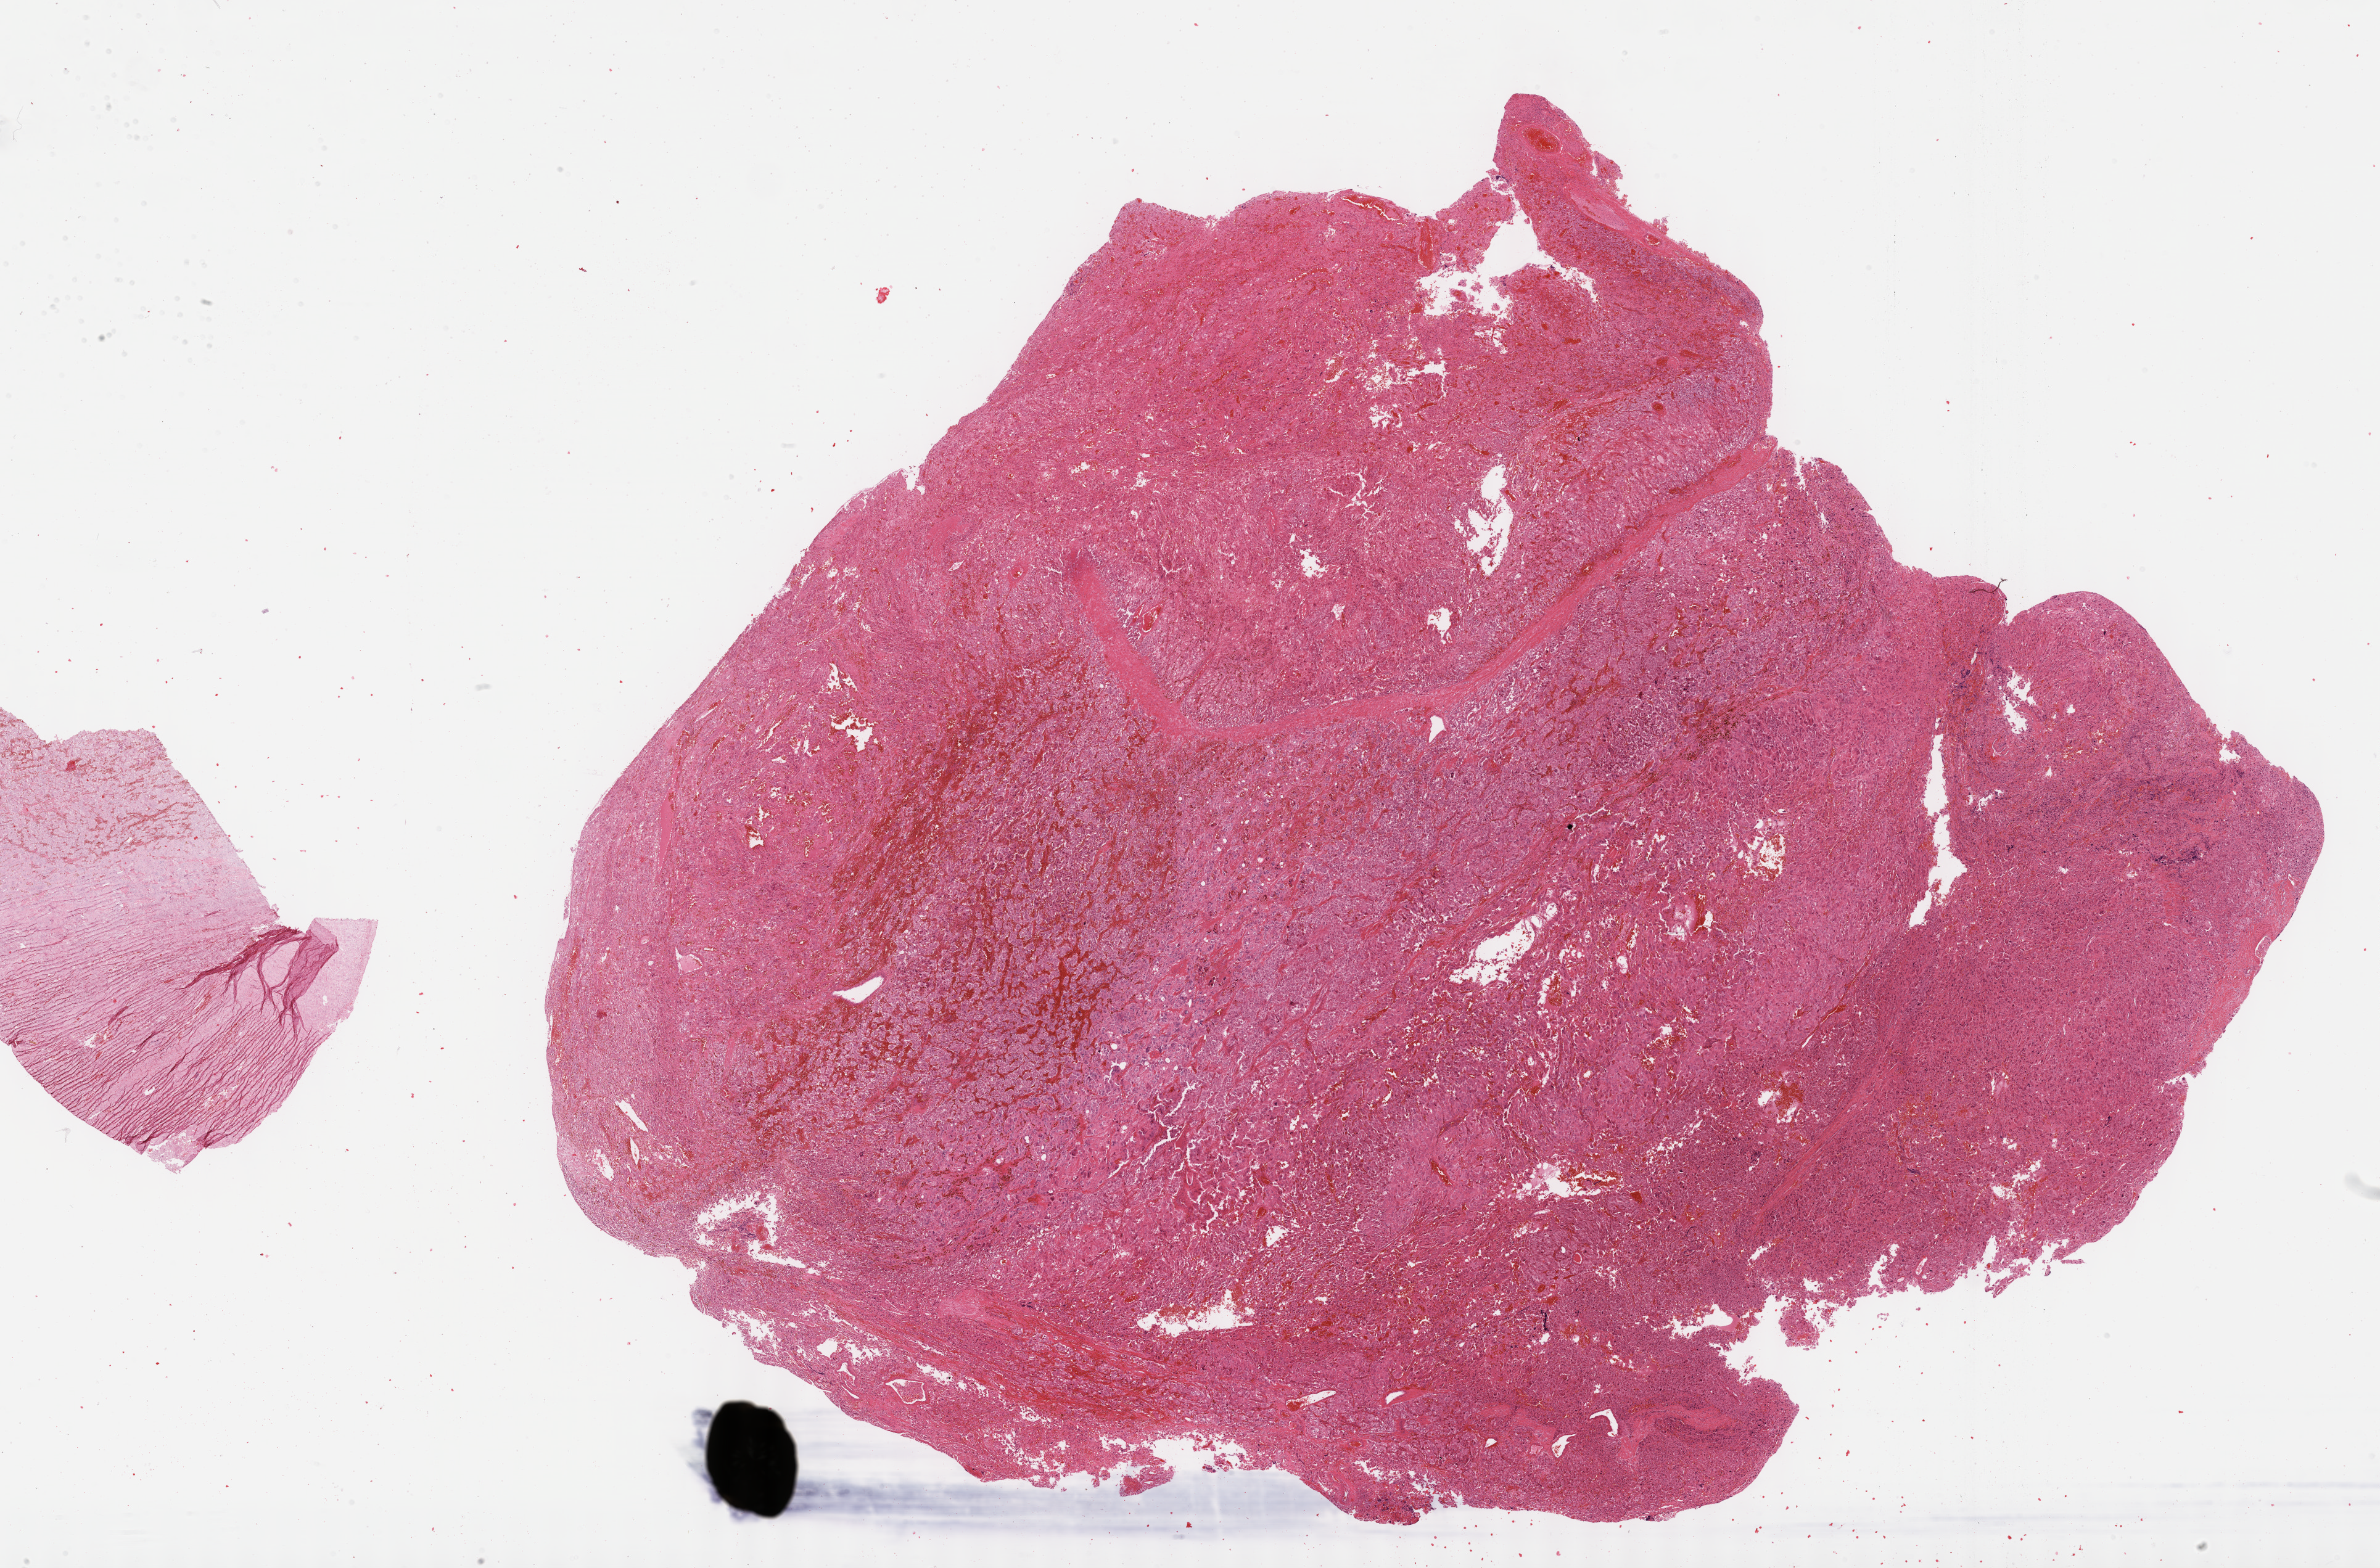
Digitized Hematoxylin and eosin (H&E) stained tissue section (whole slide) — whole scanned area (about 31.2 x 20.6 mm, from a 40x scan) shown as a low-resolution overview, formalin-fixed paraffin-embedded (FFPE) diagnostic section, adrenal gland, primary tumour sample. Male patient; age at initial diagnosis 40 years.
Laterality: right. Histologic diagnosis: Pheochromocytoma, malignant.